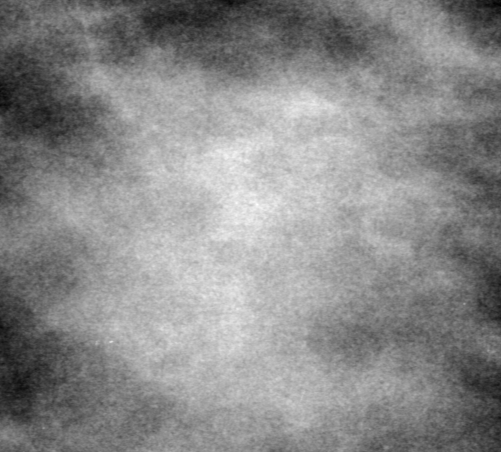
Region of interest cut from a scanned film mammogram (one marked finding), right breast, CC view.
Marked abnormality: mass, shape oval, margins obscured; BI-RADS assessment category 0 (incomplete: needs additional imaging); pathology (as recorded): benign.